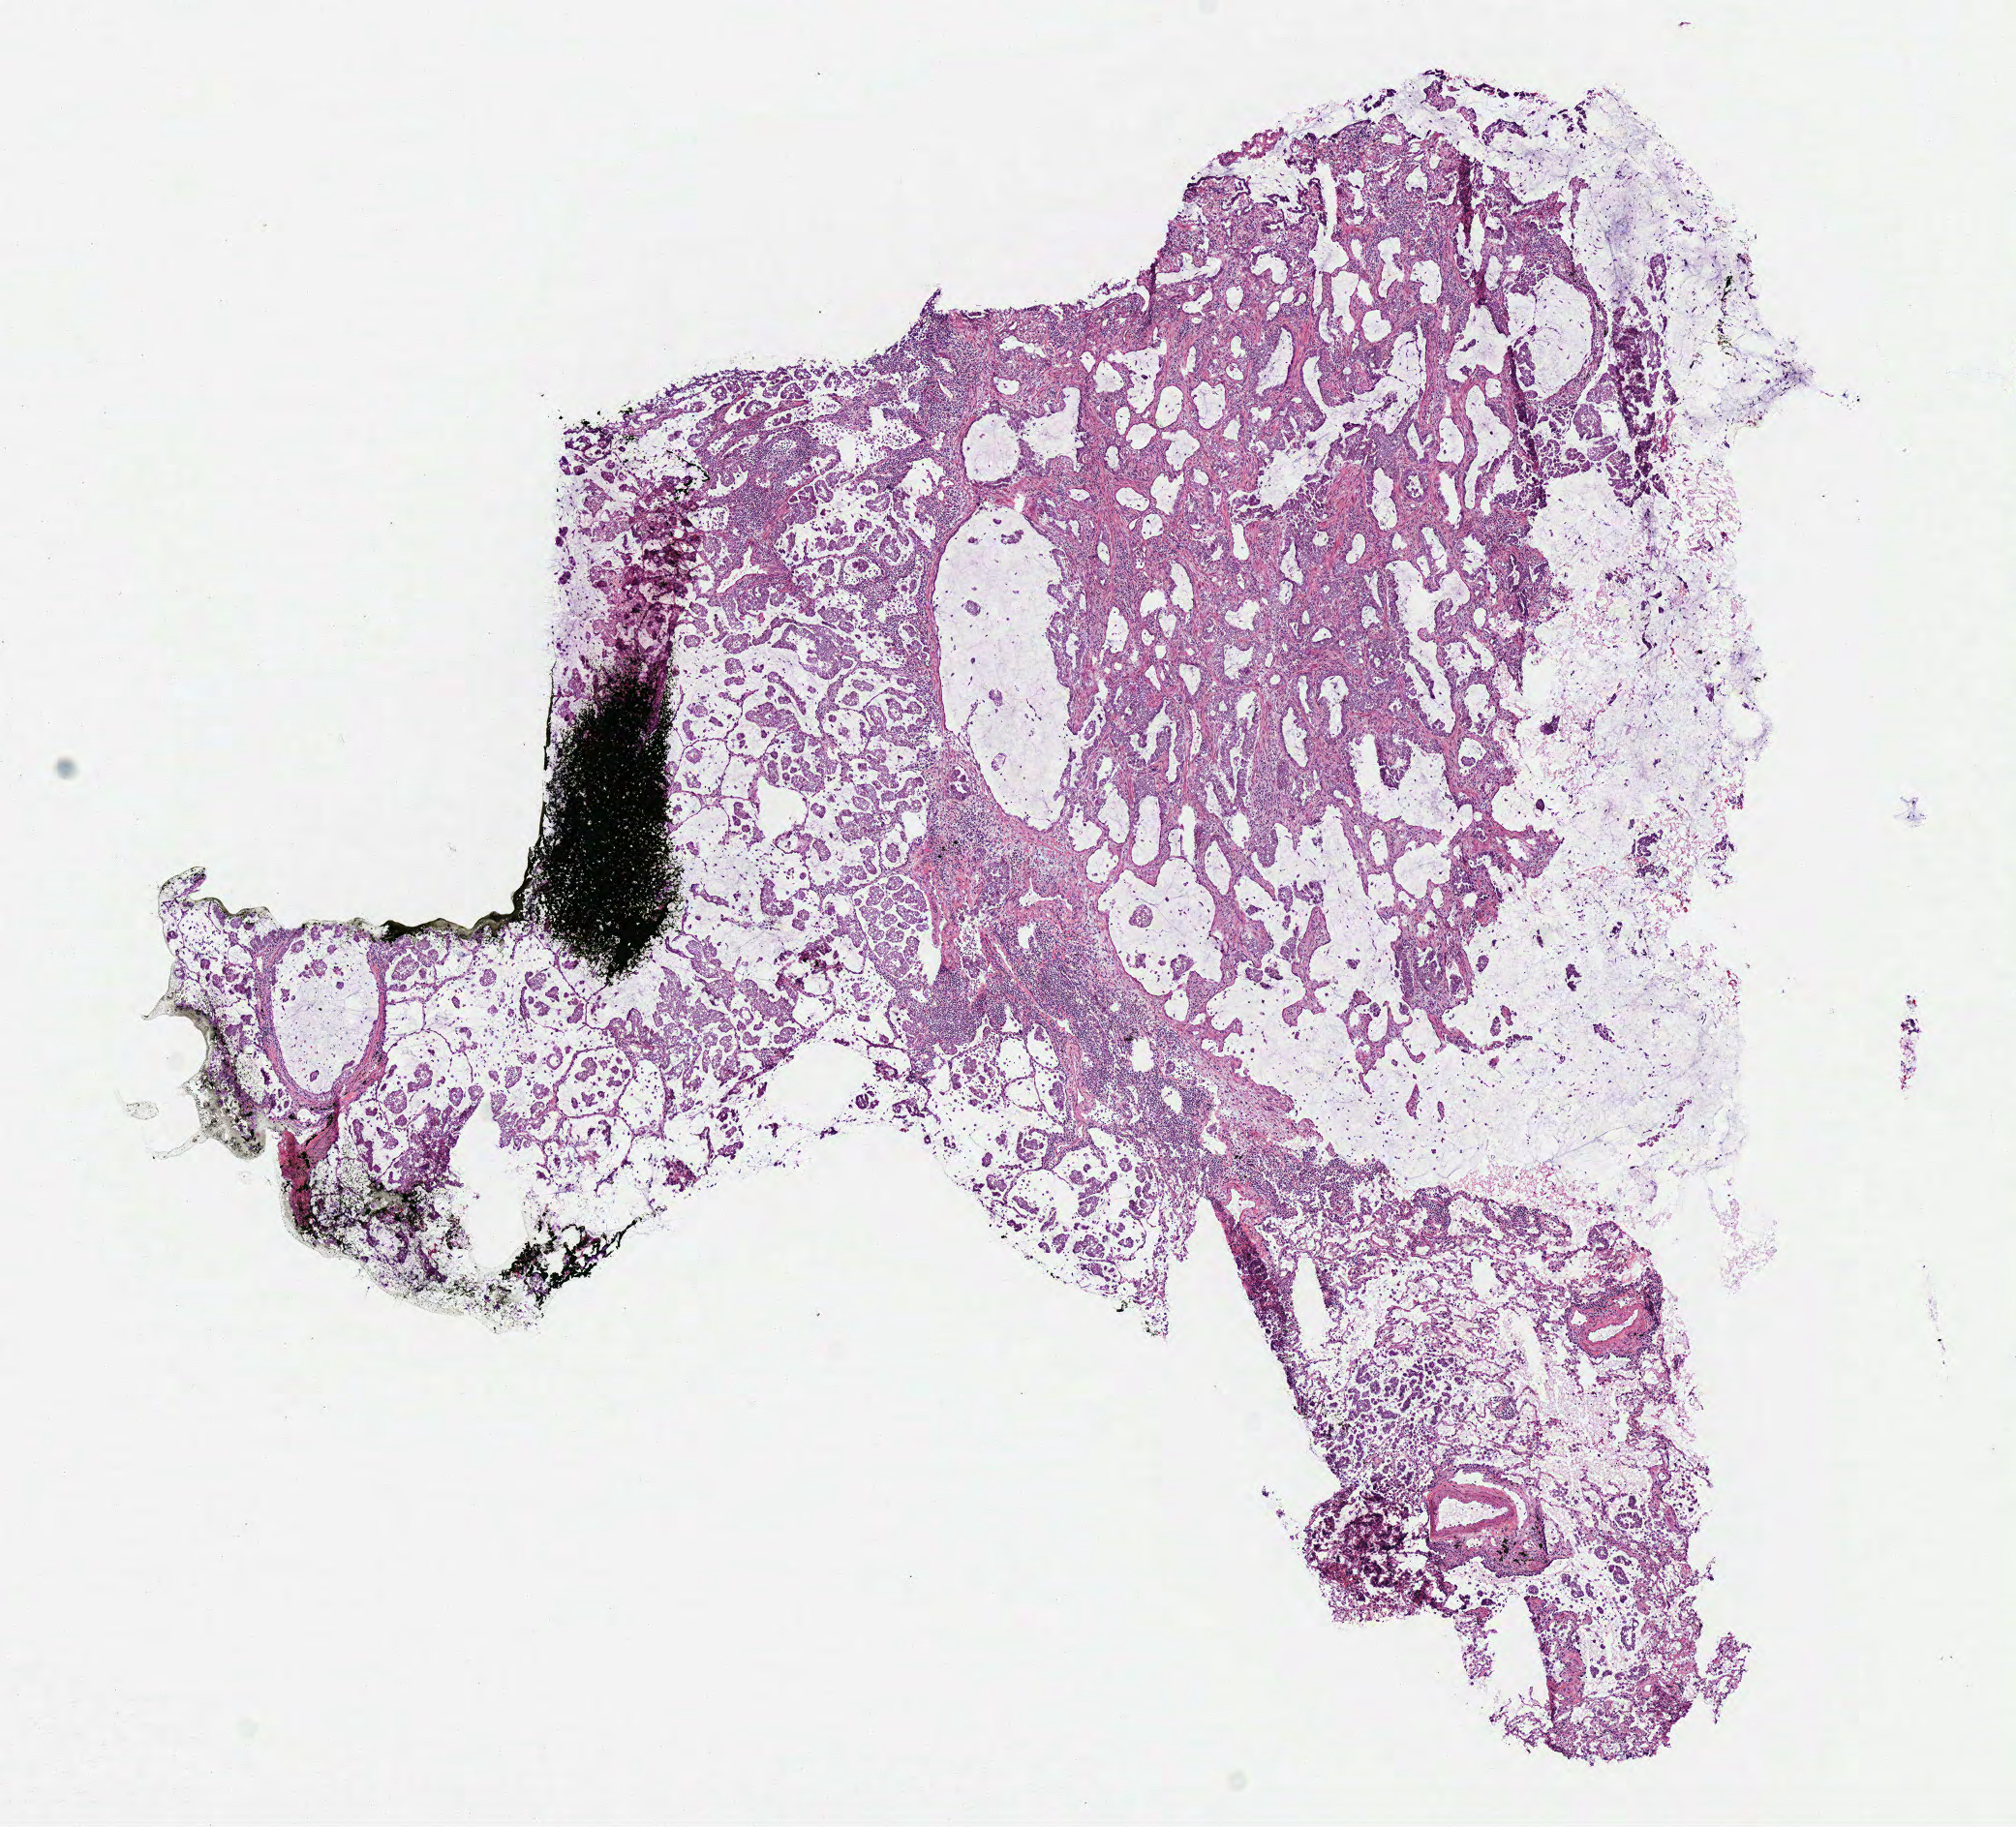
Whole-slide histology image, Hematoxylin and eosin (H&E) stained, whole scanned area (about 8.2 x 7.4 mm) shown as a low-resolution overview. Frozen section. Sample: primary tumour, lung. Male, age 61 years at initial diagnosis. Pathologist review of this section (percent, as recorded): tumour cells 85%, tumour nuclei 60%, normal cells 0%, stromal cells 15%, necrosis 0%.
Diagnosis: Adenocarcinoma with mixed subtypes. AJCC pathologic stage: IV. Laterality: right.